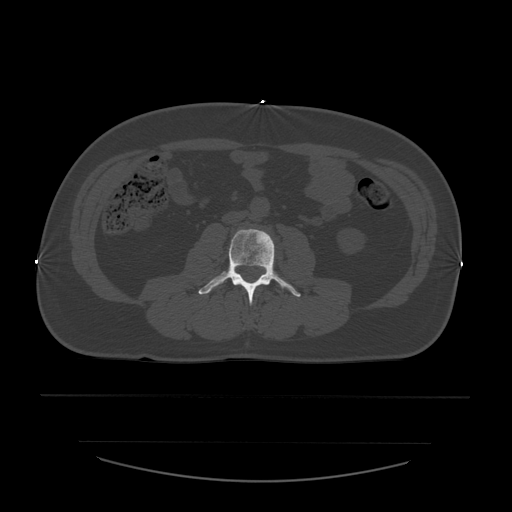
CT including the spine, one axial slice. Slice 174 of 532 in the series (ordered by position). Reconstruction kernel STANDARD. Bone window (W 1800 / L 400 HU). 512 × 512 image matrix. Patient age 44 years. From the clinical record (not read from this slice): primary cancer: soft tissue sarcoma.
Structures marked on this image (semi-automatically segmented with operator editing):
- L3 vertebra: box from (x=199, y=229) to (x=301, y=305) px